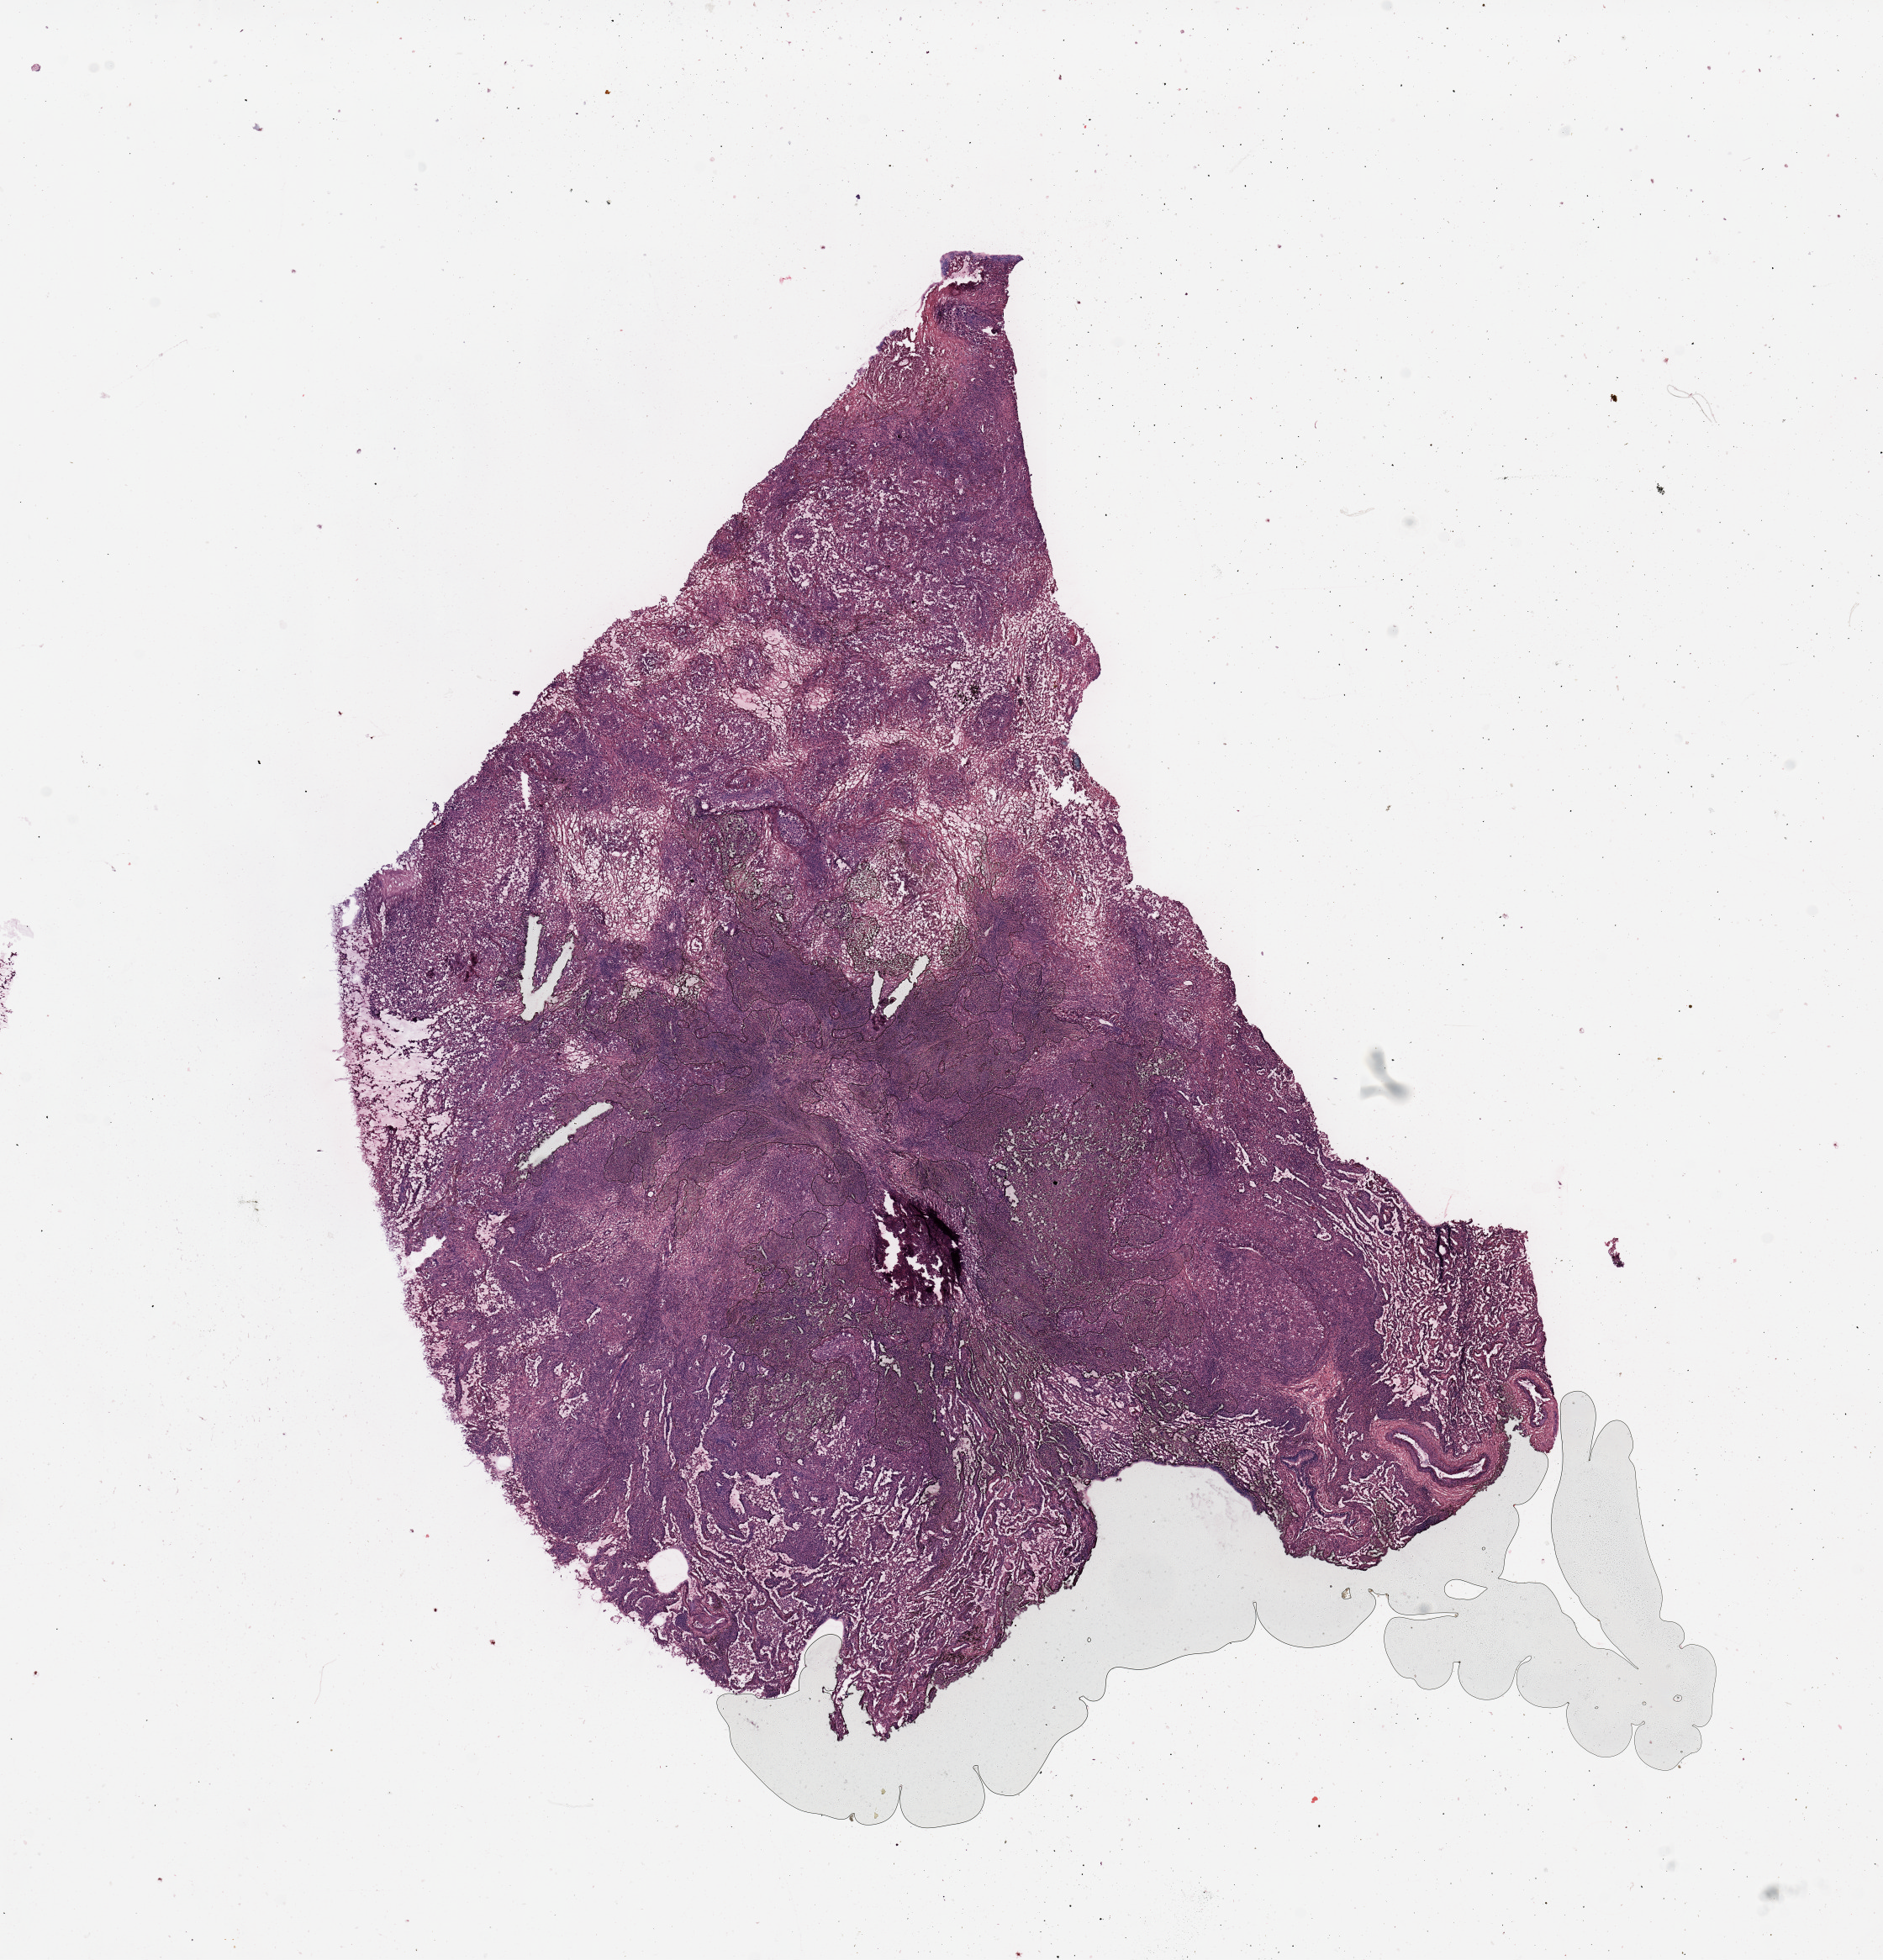
Whole-slide histology image, H&E, whole scanned area (about 17.7 x 18.4 mm, acquisition: 20x scan) shown as a low-resolution overview. Tumour tissue sample, sampled site: lung. Male, 57 y/o.
Histologic diagnosis: Adenocarcinoma, NOS.